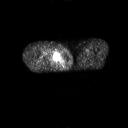
FDG PET of an extremity soft-tissue mass (from a PET/CT study), one axial slice; position 242 of 311 along the scan axis; 128 × 128 image matrix, field of view 700 × 700 mm. Patient: male, 50 years. From the clinical record (not read from this slice): histological type: undifferentiated - pleiomorphic; grade: high; site of the primary tumour: right thigh.
Outlined on this slice (expert contour drawn on MRI and transferred to this co-registered scan by the dataset authors):
- gross tumour volume including surrounding oedema: bounding box [x1, y1, x2, y2] px = [41, 49, 58, 62]
- gross tumour volume (mass): [48, 51, 58, 60]